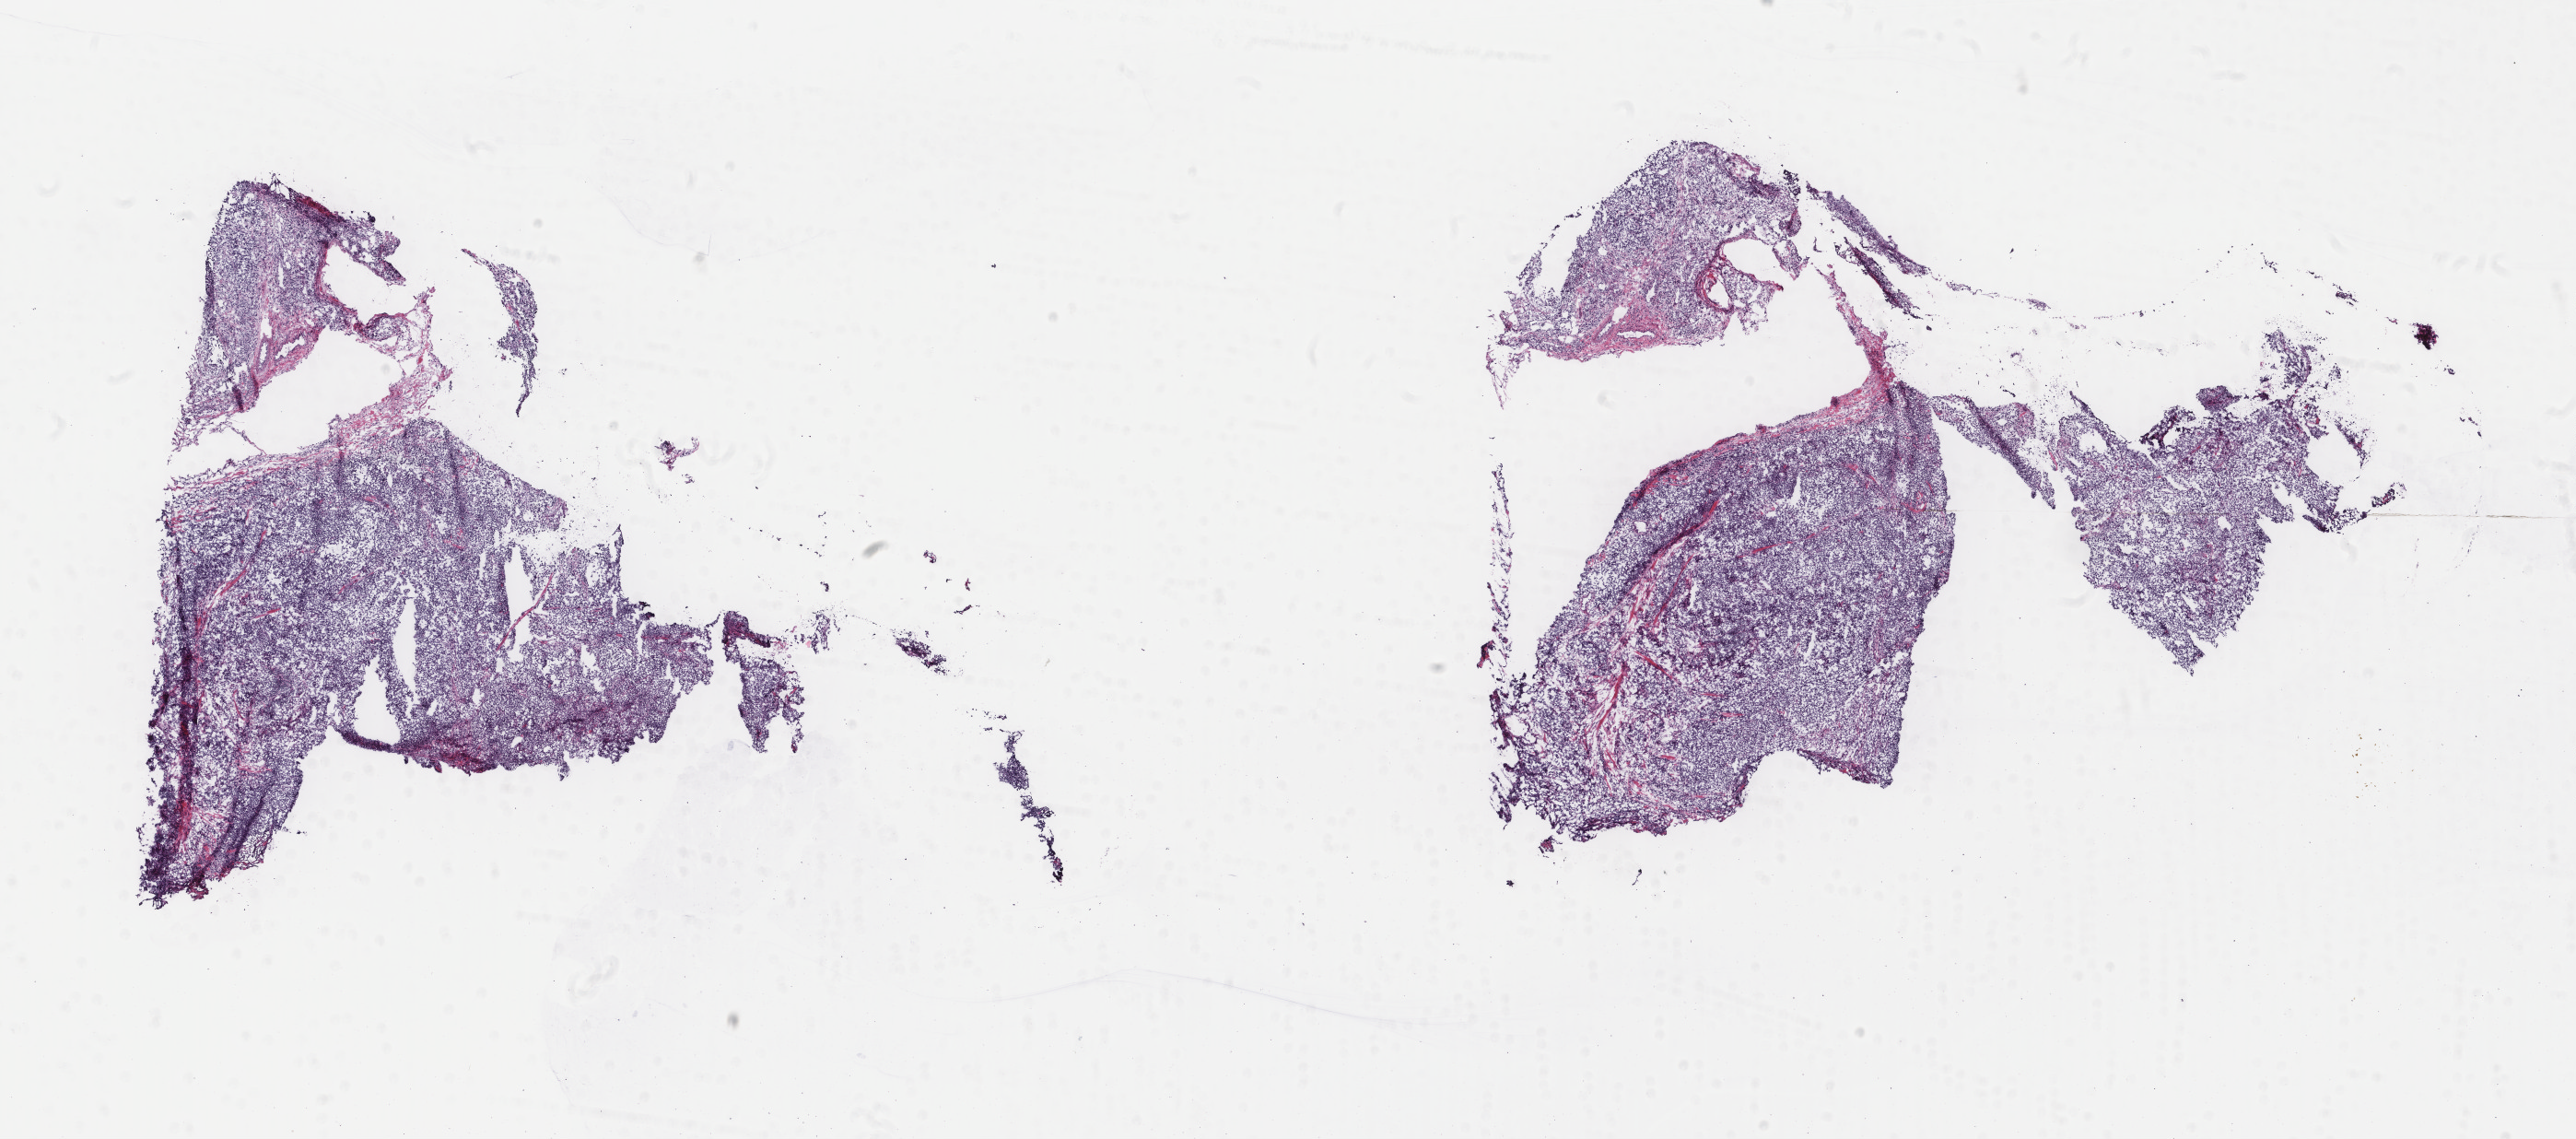
Hematoxylin and eosin (H&E) stained whole-slide image, shown as a low-resolution overview of the whole scanned area (about 22.2 x 9.8 mm), frozen section, metastatic tumour sample. Patient: female, age at initial diagnosis 46 years. Pathologist review of this section (percent, as recorded): tumour cells 100%, tumour nuclei 98%, normal cells 0%, stromal cells 0%, necrosis 0%. Inflammatory infiltration, as recorded: lymphocyte infiltration 0%, monocyte infiltration 0%, neutrophil infiltration 0%.
This section: metastatic tumour tissue. Patient diagnosis: Malignant melanoma, NOS.